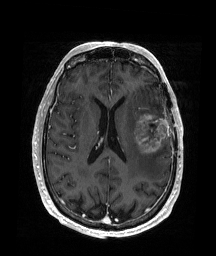
Brain MRI from a brain-tumour surgery series, one axial slice. T1-weighted post-contrast. 1 mm slice thickness. 216 × 256 image matrix, field of view 219 × 260 mm. Case-level facts recorded for this patient, not image findings: histopathology: Glioblastoma; WHO grade: 4; IDH mutation: no; tumour location: Left Frontal.
Structures marked on this image (manually delineated by an expert):
- tumour: box from (x=134, y=113) to (x=169, y=155) px